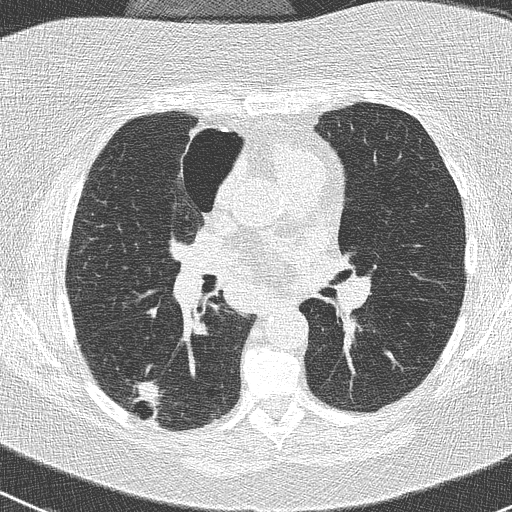
Low-dose screening chest CT, one axial slice. Position 142 of 261 along the scan axis. Reconstruction kernel B50f. Lung window (W 1500 / L -600 HU). 512 × 512 image matrix.
Annotated regions visible in this slice (expert manual segmentation):
- lesion 1 (tumor, lower lobe of right lung): box from (x=133, y=381) to (x=162, y=408) px